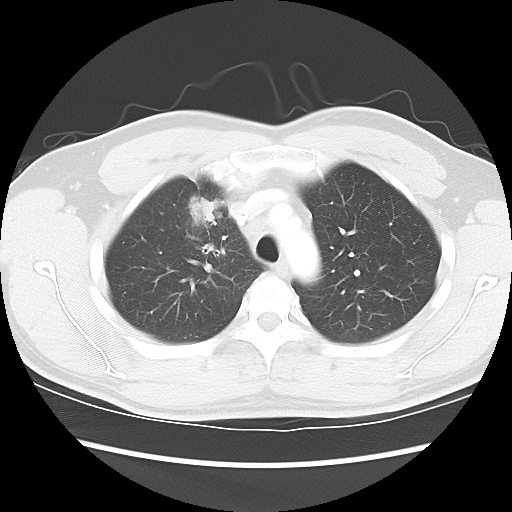
Chest CT, one axial slice; position 67 of 80 along the scan axis; reconstruction kernel LUNG; 120 kVp; lung window (W 1500 / L -600 HU); 5 mm slice thickness; 512 × 512 image matrix, field of view 360 × 360 mm. Male patient, age 35 years. Case-level facts recorded for this patient, not image findings: clinical TNM (as recorded): T1c N1 M1b.
Annotated regions visible in this slice (rectangle marked by the reading radiologist):
- lung tumour (recorded histology: adenocarcinoma): bounding box (x1, y1, x2, y2) in pixels: (184, 189, 225, 229)